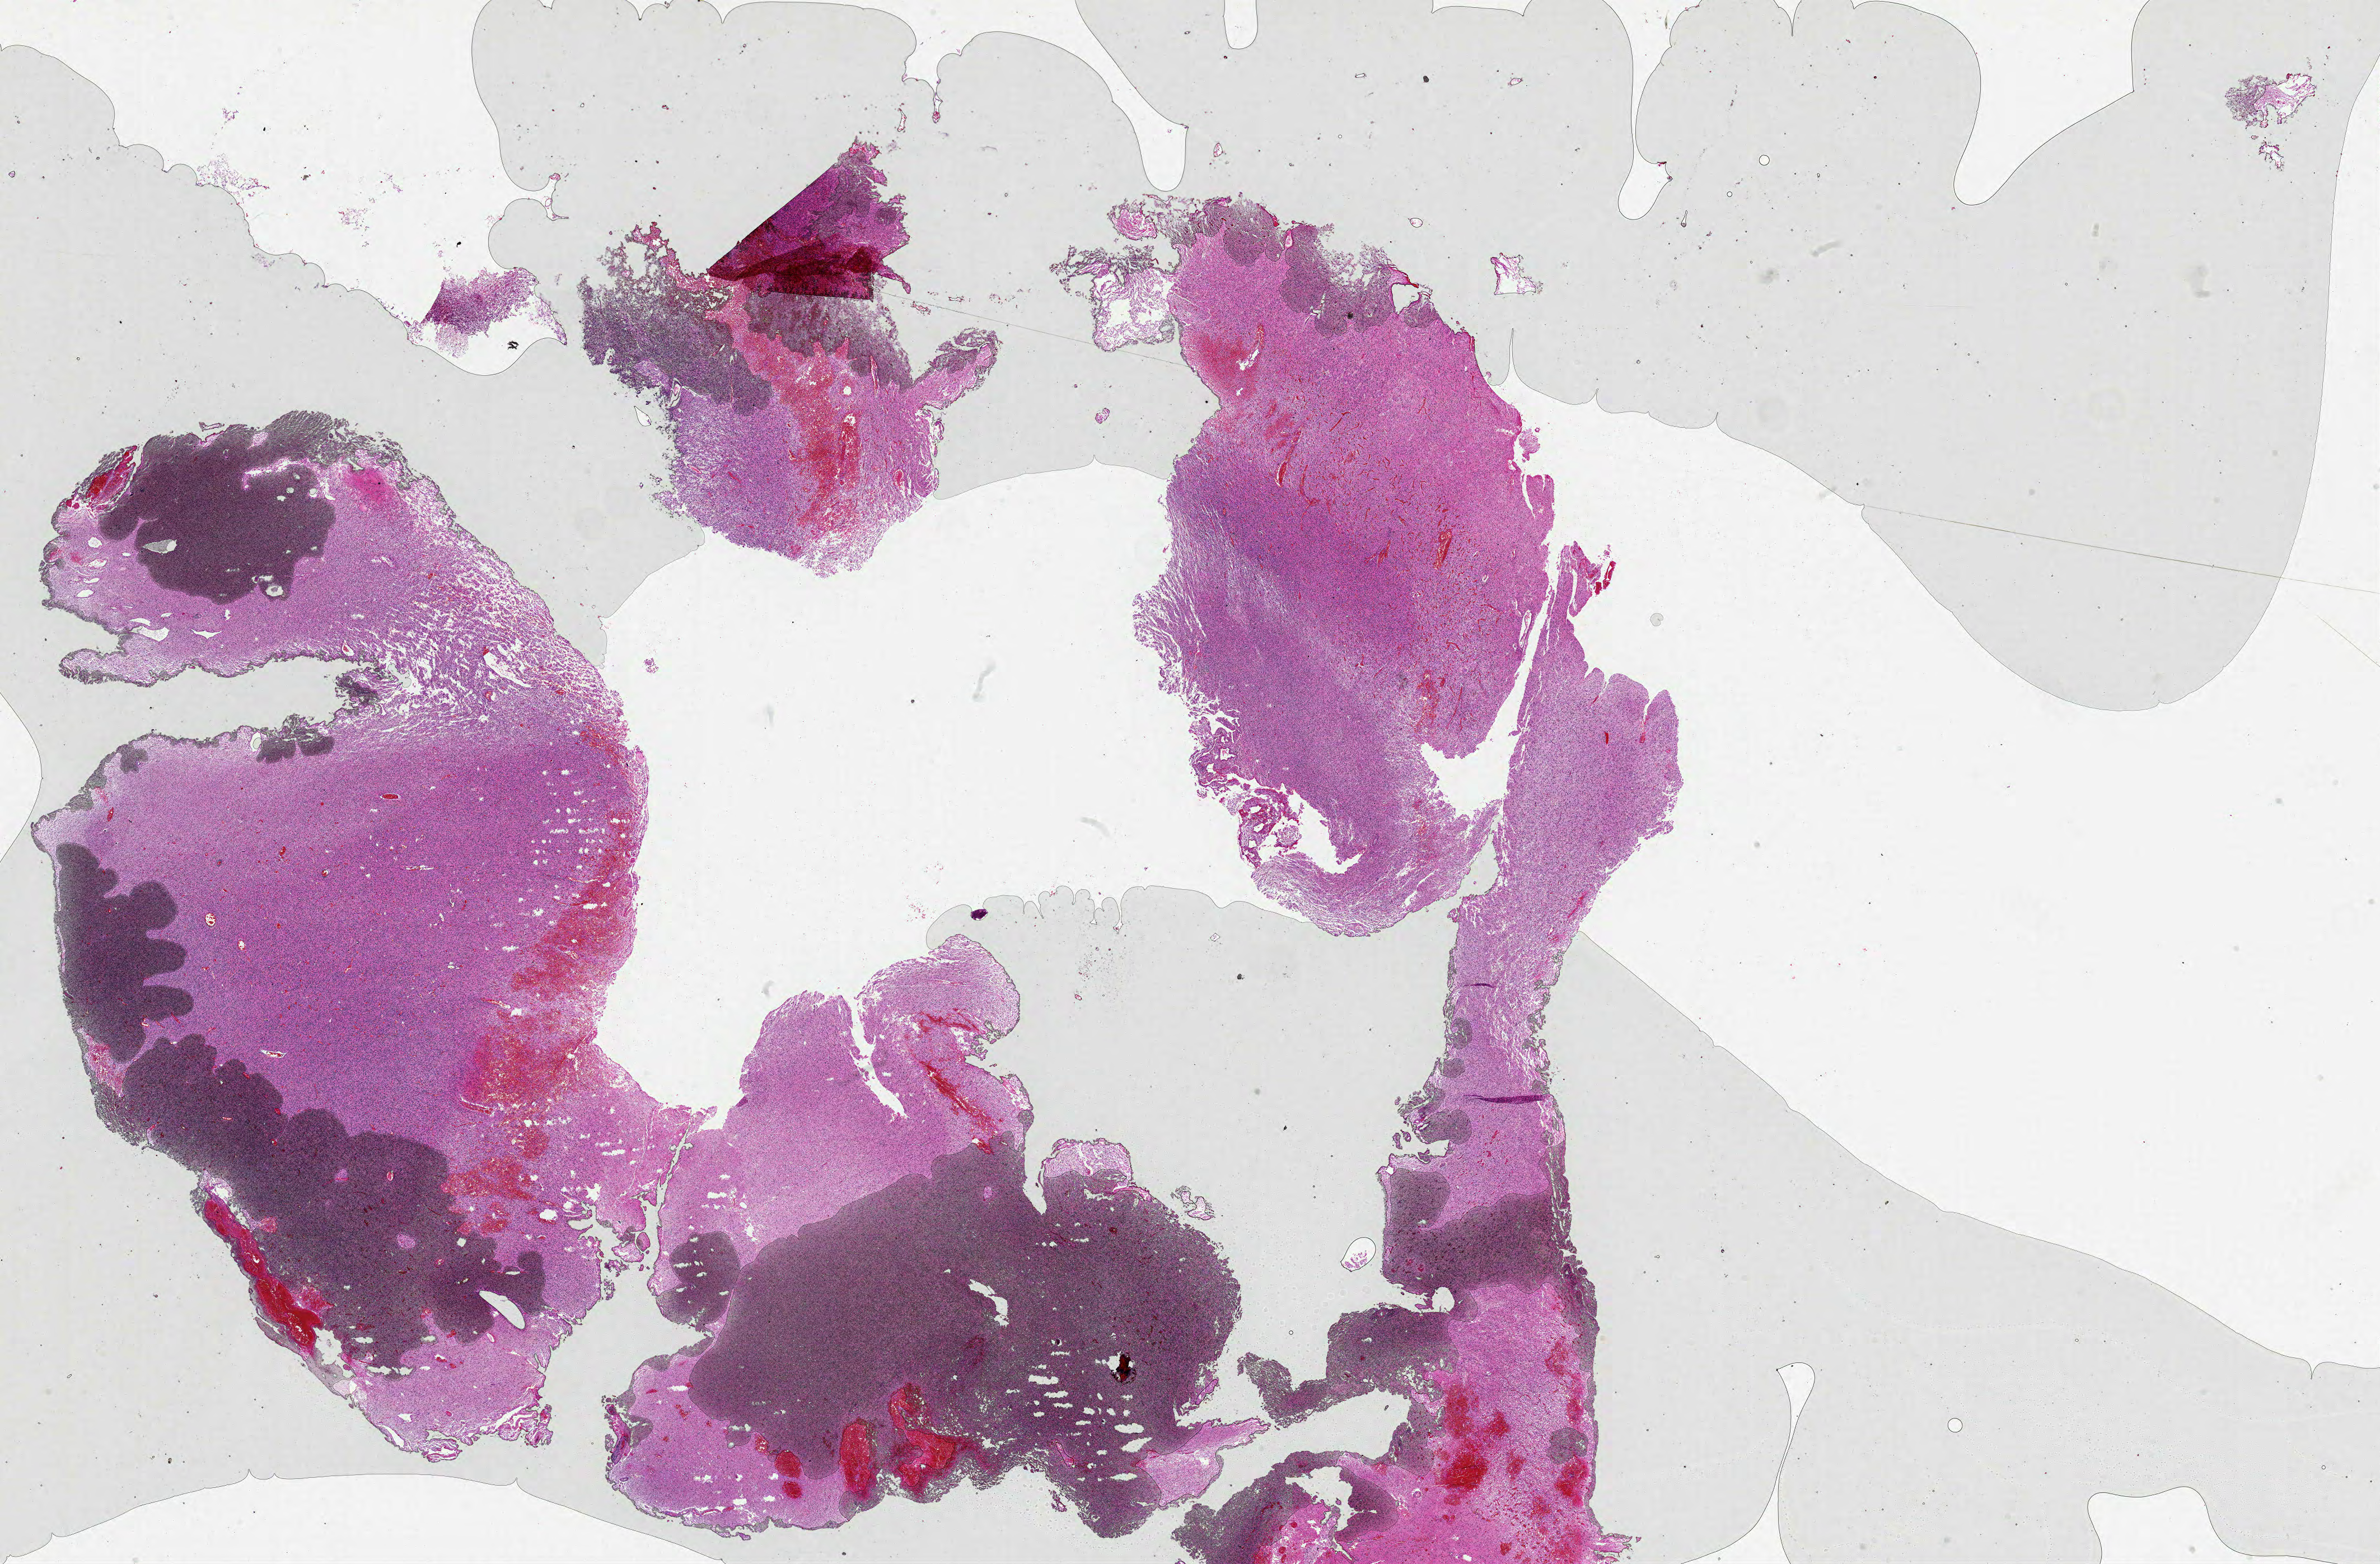
Digitized H&E tissue section (whole slide), a low-resolution overview of the entire scanned area, about 34.0 x 22.3 mm. Formalin-fixed paraffin-embedded (FFPE) diagnostic section. Brain, primary tumour sample. Male patient; age at initial diagnosis 52 years.
Histologic diagnosis: Glioblastoma.